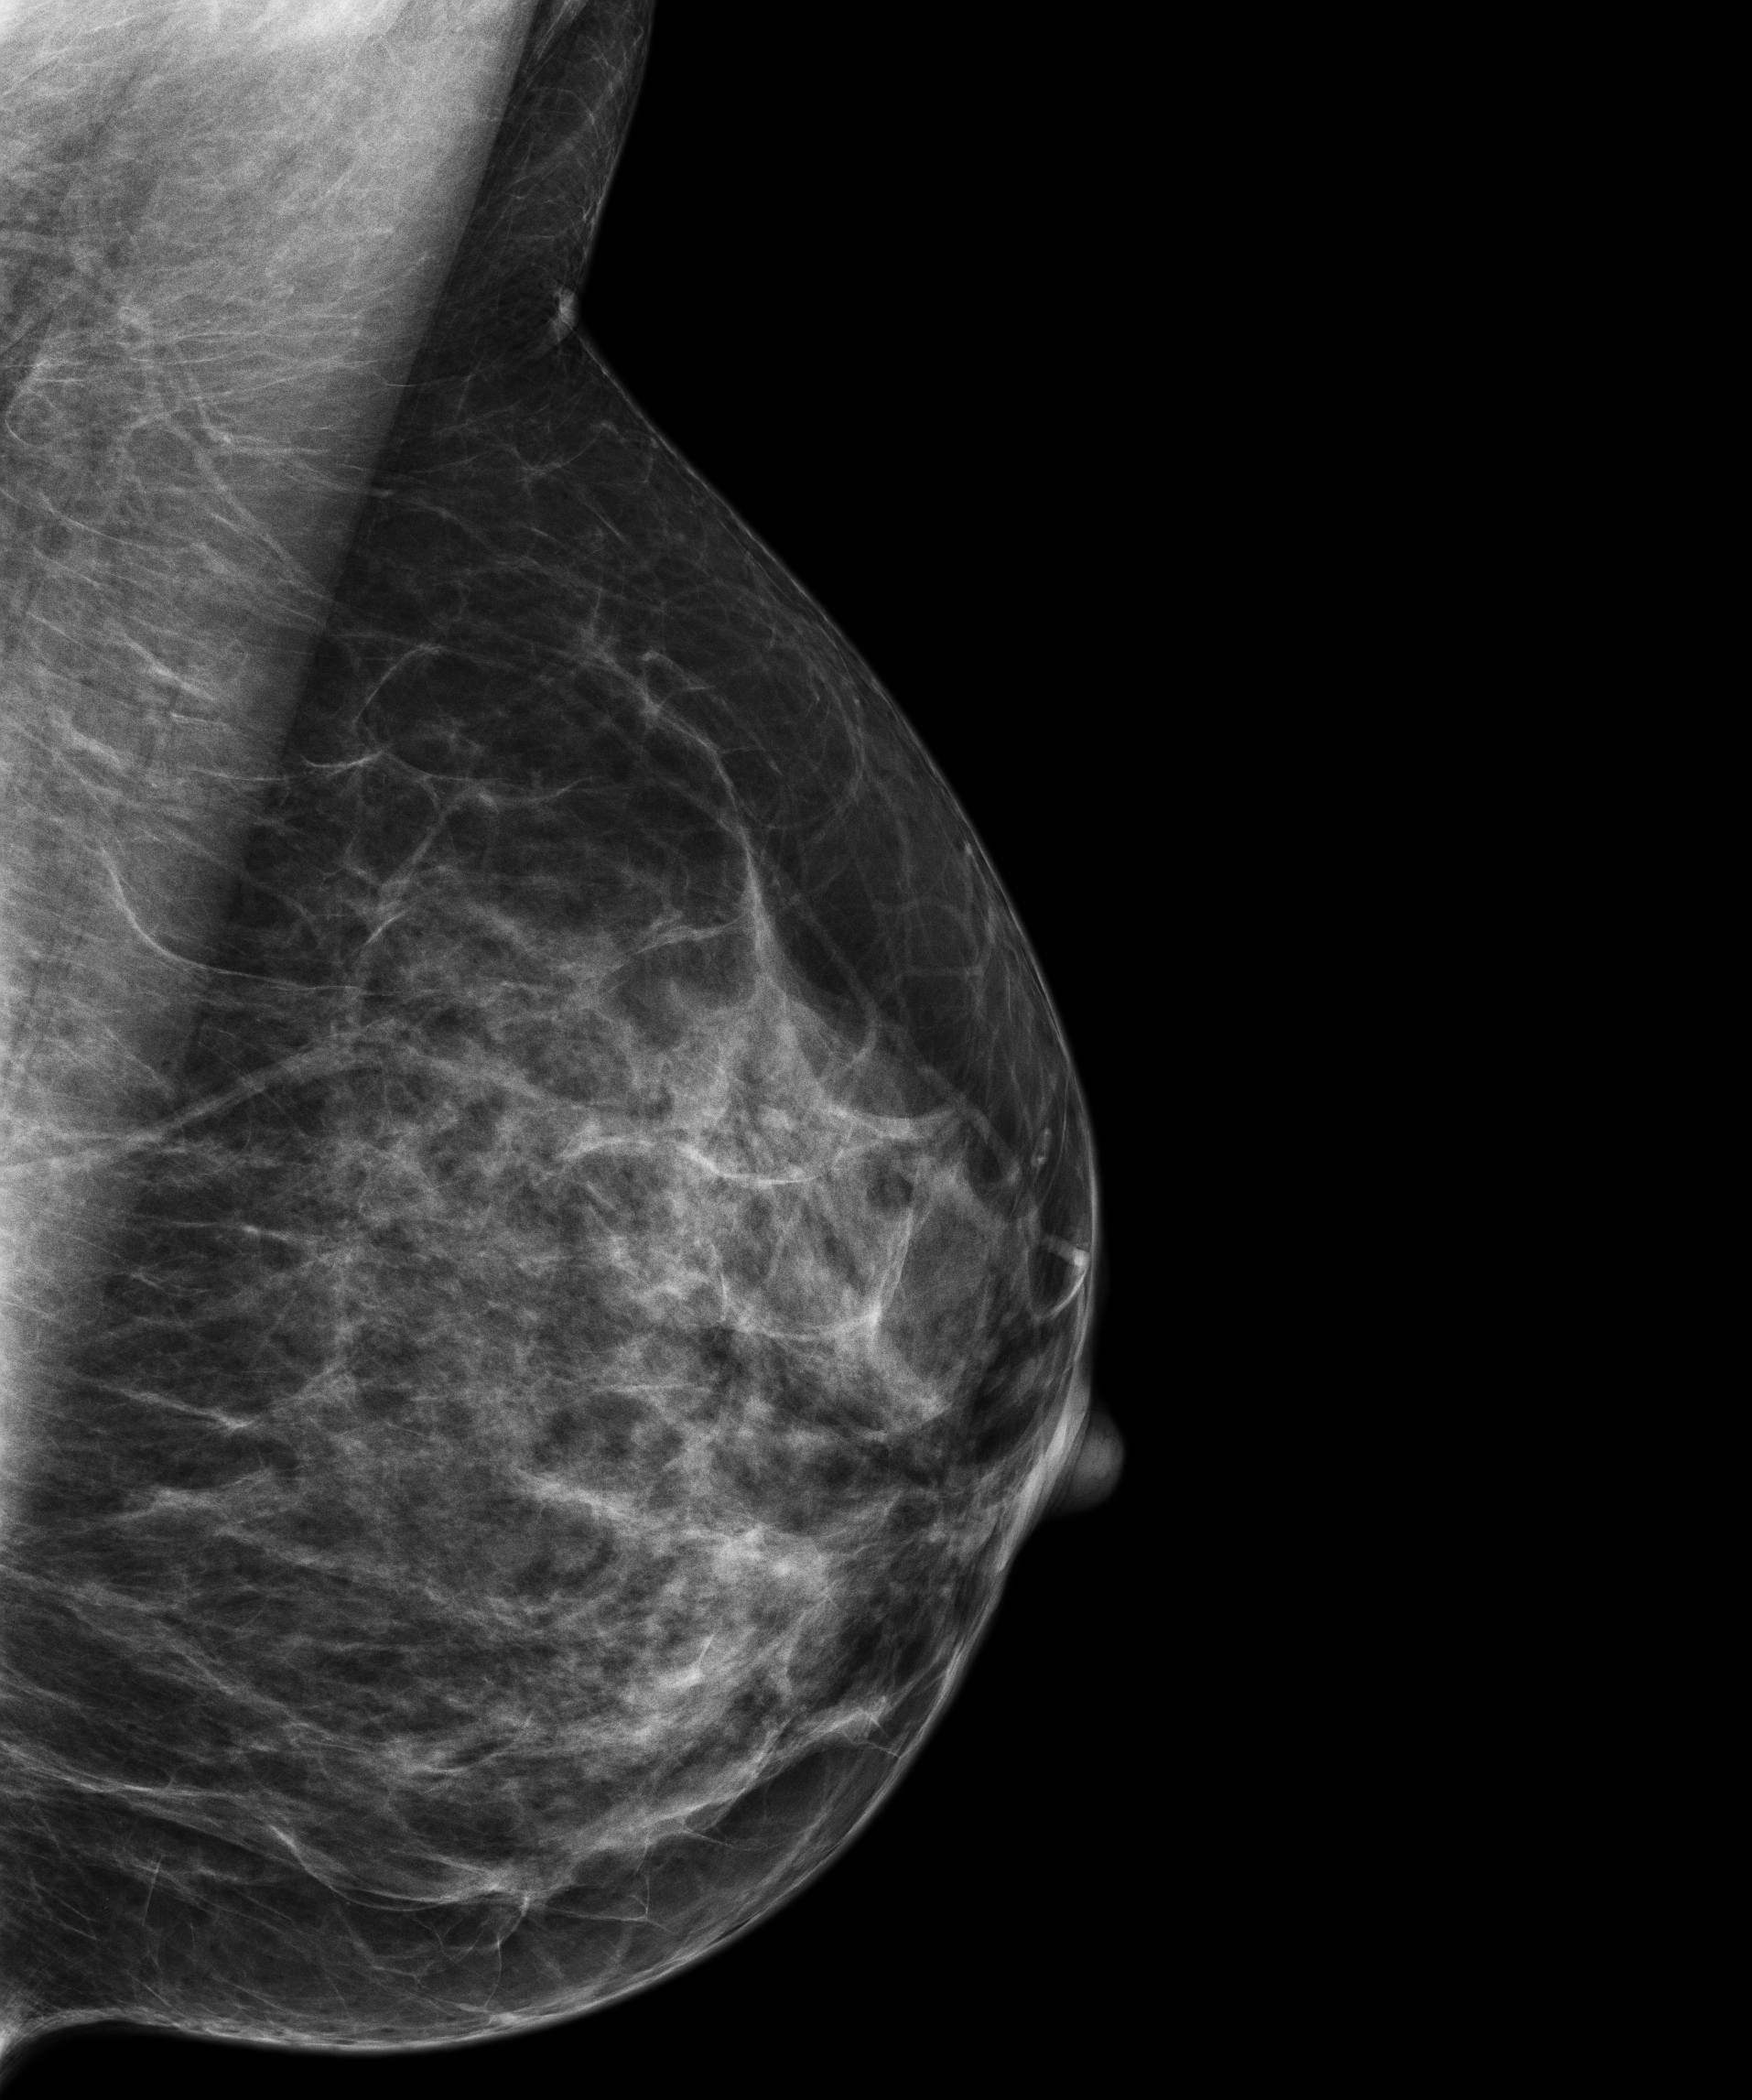
Full-field digital mammogram (FFDM); left breast; medio-lateral oblique projection; screening examination. Patient aged 53 years (female).
Final BI-RADS assessment for this screening round (tomosynthesis exam, both breasts): category 1.